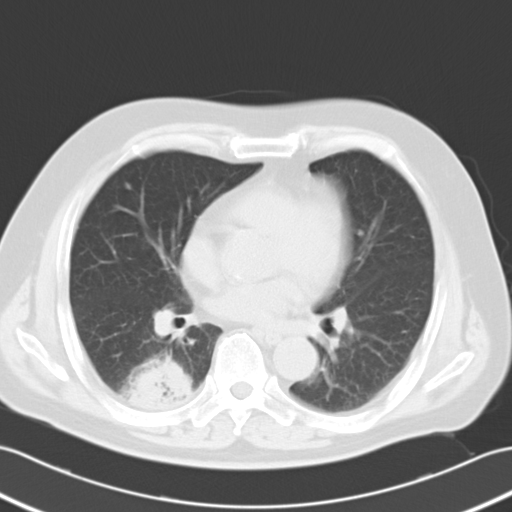
Chest CT, one axial slice. Lung window (W 1500 / L -600 HU). 10 mm slice thickness. 512 × 512 image matrix, field of view 353 × 353 mm. Patient: male, 70 years. From the clinical record (not read from this slice): clinical TNM (as recorded): T2 N0 M0; histopathological grade: G2.
Structures marked on this image (rectangle marked by the reading radiologist):
- lung tumour (recorded histology: adenocarcinoma): bounding box [x1, y1, x2, y2] px = [125, 353, 195, 418]